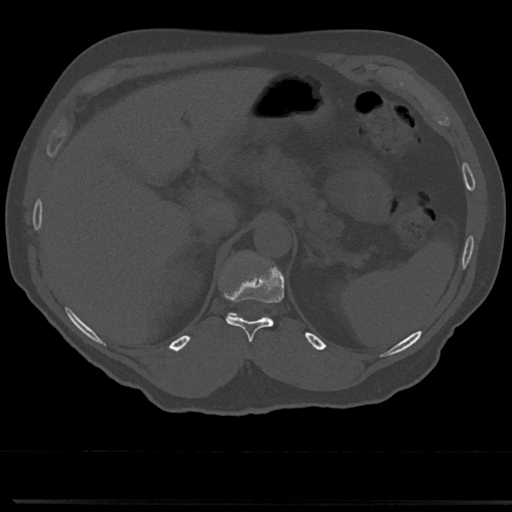
CT including the spine, one axial slice. Position 188 of 817 along the scan axis. Bone window (W 1800 / L 400 HU). 0.5 mm slice thickness. 512 × 512 image matrix, field of view 355 × 355 mm. Patient: male, 61 years. Case-level facts recorded for this patient, not image findings: primary cancer: prostate.
Annotated regions visible in this slice (semi-automatically segmented with operator editing):
- T11 vertebra: bounding box <226,274,283,344> (left, top, right, bottom; pixels)
- T12 vertebra: <226,255,283,320>